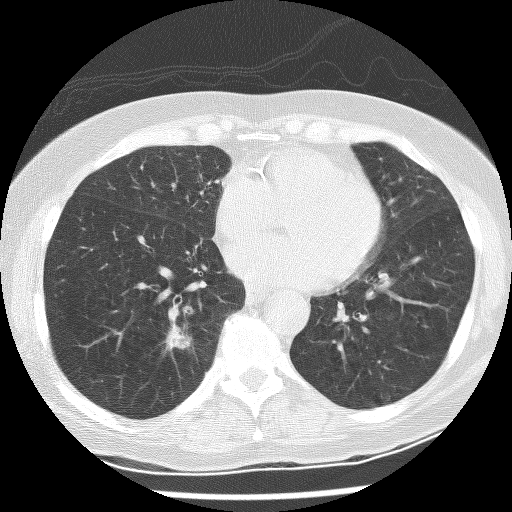
Chest CT (low-dose screening protocol), one axial image; baseline screening round; lung window (W 1500 / L -600 HU); 512 × 512 image matrix, field of view 300 × 300 mm. Female participant, aged 60 years at enrolment. Former smoker at enrolment.
- Expert reader's lesion annotation, box from (x=156, y=322) to (x=203, y=358) px.
- The exam's reader record, not a measurement of the box and not confirmed to be the same lesion: non-calcified nodule or mass ≥4 mm, right lower lobe, 10 × 6 mm, spiculated (stellate) margins, mixed attenuation.
- Participant outcome: lung cancer diagnosed 275 days after this screen — adenocarcinoma with squamous metaplasia, right lower lobe, poorly differentiated (G3), stage IA (AJCC 6th edition), 23 mm at pathology.